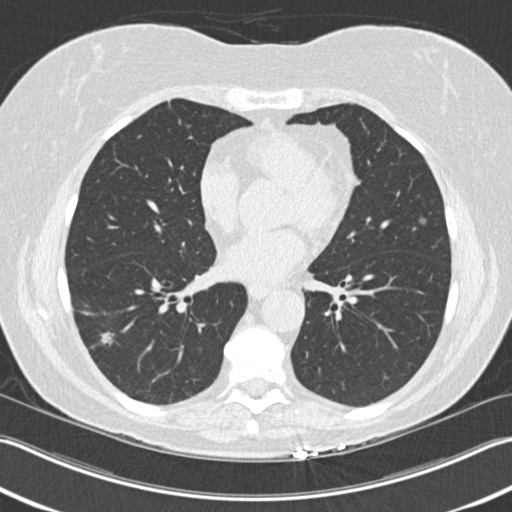
Chest CT (low-dose screening protocol), one axial image. First (baseline) screen. Lung window (W 1500 / L -600 HU). 512 × 512 image matrix, field of view 348 × 348 mm. Female, age 63 years at enrolment. Current smoker at enrolment.
• Expert-annotated lung lesion, bounding box <64,305,131,369> (left, top, right, bottom; pixels).
• The screening reader recorded 3 non-calcified nodules or masses ≥4 mm on this exam (right upper lobe, right lower lobe, right lower lobe); which of them this box marks is not recorded.
• Official screen result: positive, change unspecified: nodule(s) >= 4 mm or enlarging nodule(s), mass(es), or other non-specific abnormalities suspicious for lung cancer.
• Later outcome: lung cancer diagnosed 57 days after this screen — bronchiolo-alveolar adenocarcinoma, NOS, right lower lobe, well differentiated (G1), stage IA (AJCC 6th edition), 25 mm at pathology.